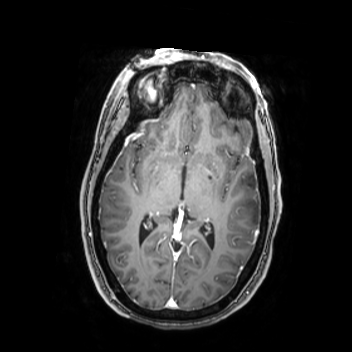
Brain MRI from a brain-tumour surgery series, one axial slice; T1-weighted post-contrast; 352 × 352 image matrix. From the clinical record (not read from this slice): histopathology: Oligodendroglioma; WHO grade: 2; IDH mutation: yes; tumour location: Left Middle Temporal Gyrus.
Outlined on this slice (manually delineated by an expert):
- tumour: bounding box (x1, y1, x2, y2) in pixels: (224, 176, 262, 225)